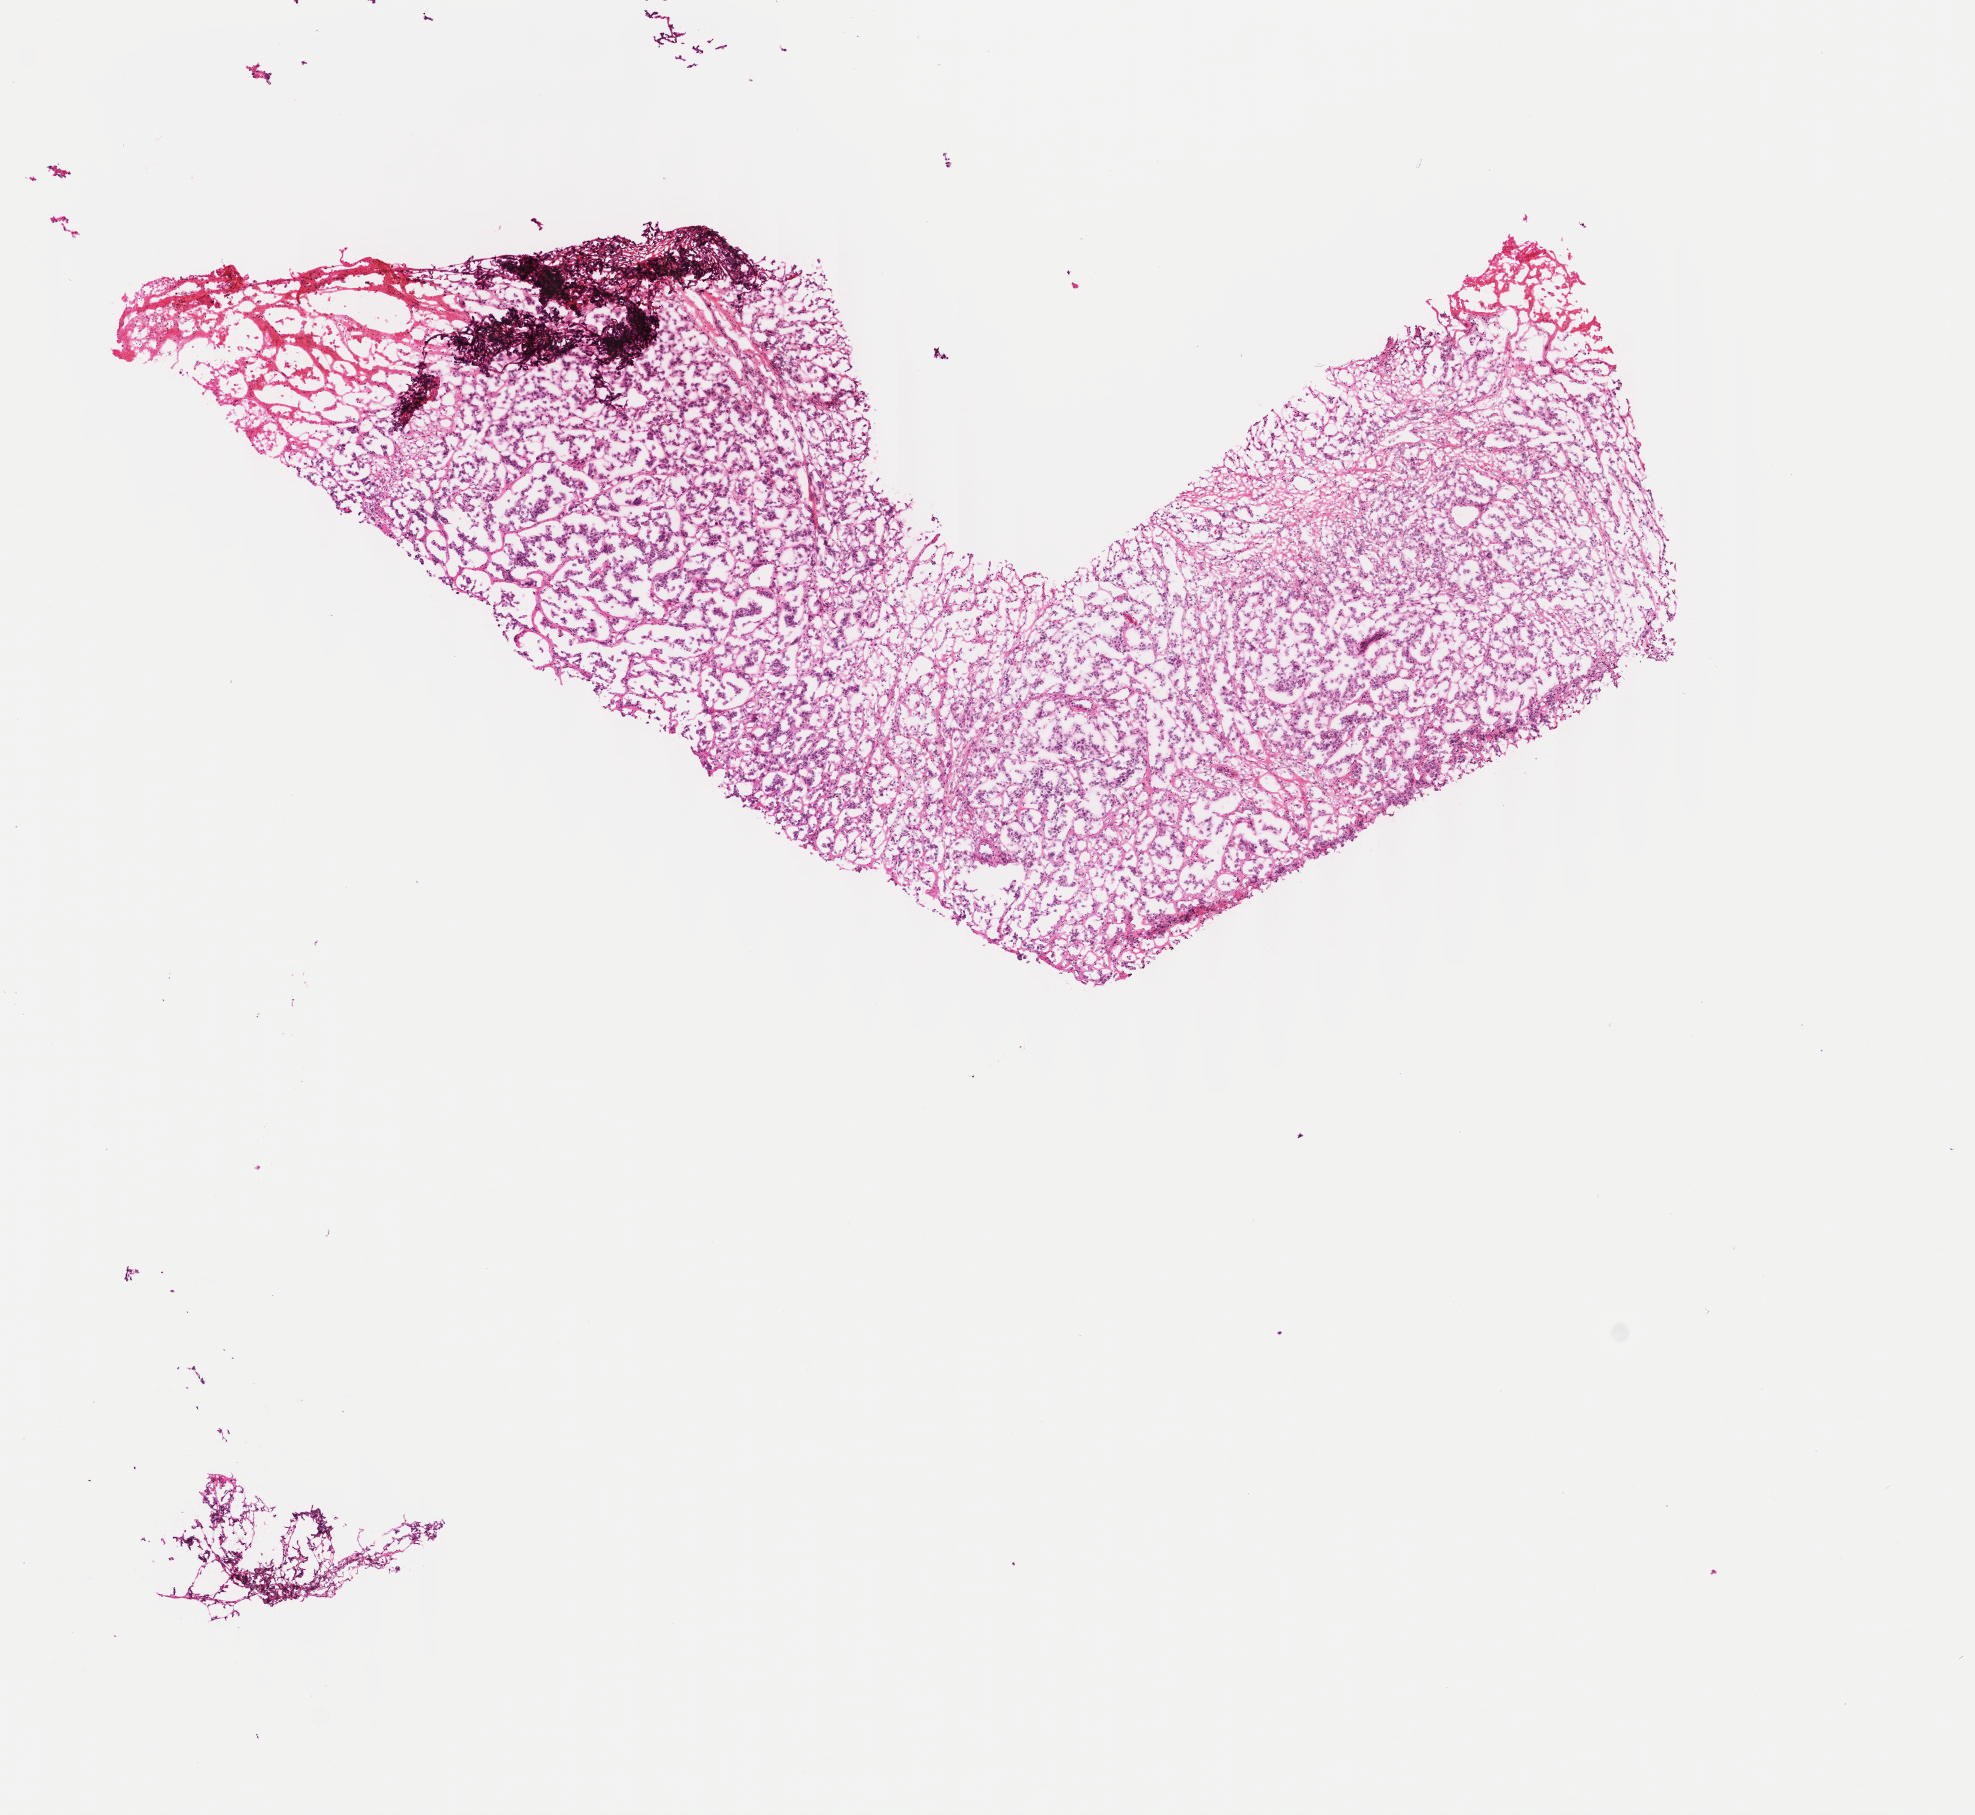
H&E whole-slide image, whole scanned area (about 7.9 x 7.2 mm, acquisition: 40x scan) shown as a low-resolution overview. Frozen section. Metastatic tumour sample, sampled site not recorded. Patient: male, age at initial diagnosis 74 years. Composition of this section per pathologist review: tumour cells 90%, tumour nuclei 85%, normal cells 0%, stromal cells 10%, necrosis 0%. Inflammatory infiltration, as recorded: lymphocyte infiltration 0%, monocyte infiltration 0%, neutrophil infiltration 0%.
This section: metastatic tumour tissue. Patient diagnosis: Malignant melanoma, NOS.